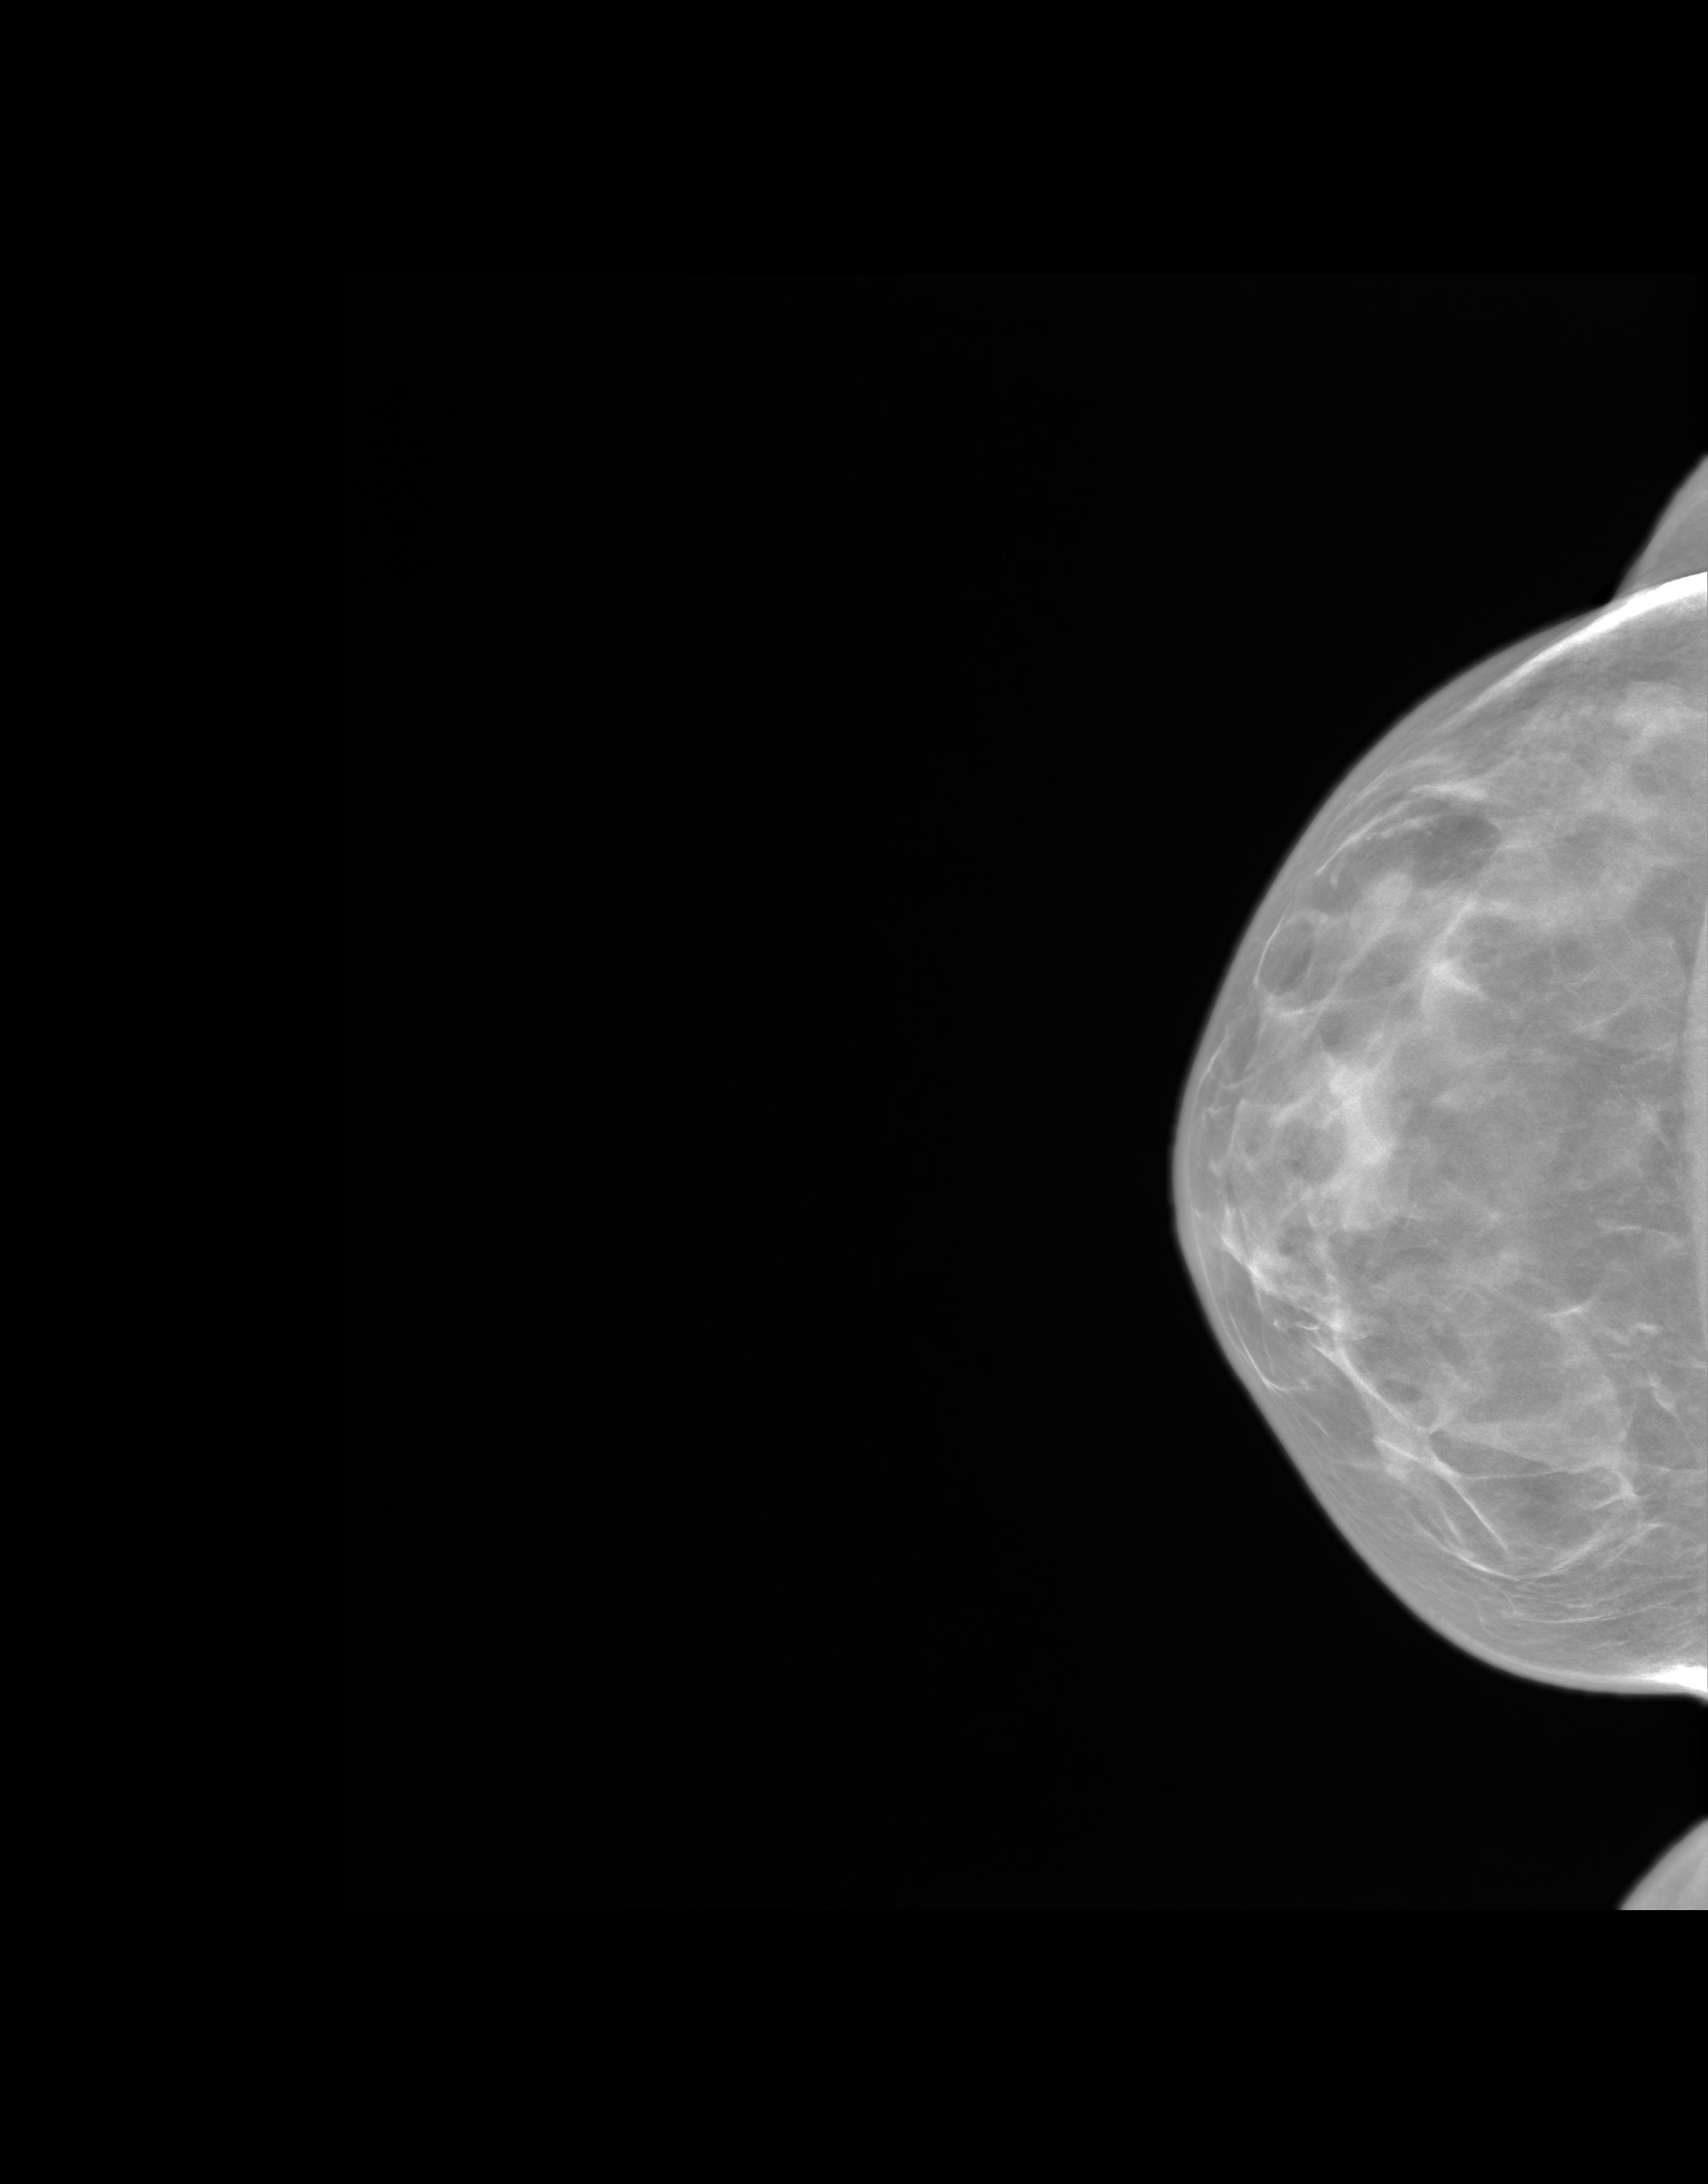
Screening examination. Female patient, age 67 years.
Image type: synthesized 2-D view from tomosynthesis. Breast: right. Projection: craniocaudal (CC) view.